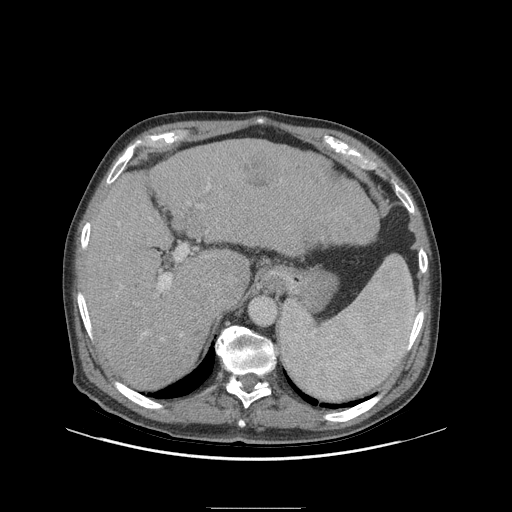
Contrast-enhanced abdominal CT (liver protocol), one axial slice; slice 68 of 105 in the series (ordered by position); reconstruction kernel STANDARD; soft-tissue window (W 400 / L 40 HU); 2.5 mm slice thickness; 512 × 512 image matrix, field of view 440 × 440 mm. From the clinical record (not read from this slice): diagnosis: hepatocellular carcinoma (patient treated with transarterial chemoembolisation; whether this scan precedes or follows treatment is not stated here); TNM stage (as recorded): Stage-I; Child-Pugh class: A; tumour nodularity: uninodular; tumour size: 5.1 cm.
Outlined on this slice (semi-automatically segmented with operator editing):
- liver parenchyma outside the tumour (the mass and vessels are separate outlines, so this box may not span the whole liver): bounding box <80,138,378,389> (left, top, right, bottom; pixels)
- mass: <237,156,279,187>
- liver vessels: <91,183,211,340>